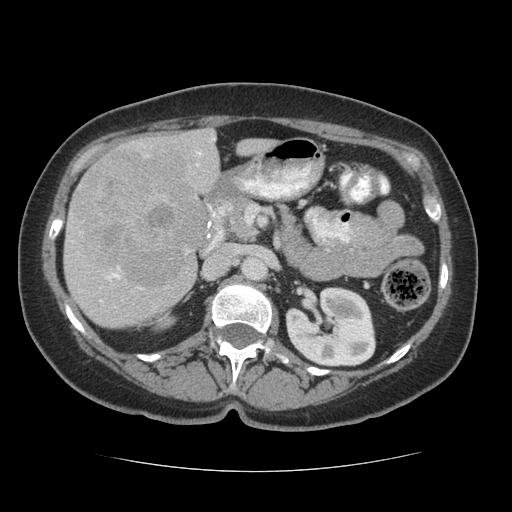
Contrast-enhanced abdominal CT (liver protocol), one axial slice; reconstruction kernel STANDARD; 140 kVp; soft-tissue window (W 400 / L 40 HU); 2.5 mm slice thickness; 512 × 512 image matrix. Case-level facts recorded for this patient, not image findings: diagnosis: hepatocellular carcinoma (patient treated with transarterial chemoembolisation; whether this scan precedes or follows treatment is not stated here); TNM stage (as recorded): Stage-I; Child-Pugh class: A; tumour differentiation: moderately differentiated; tumour nodularity: uninodular.
Outlined on this slice (semi-automatic segmentation, software-assisted and operator-edited):
- liver parenchyma outside the tumour (the mass and vessels are separate outlines, so this box may not span the whole liver): bounding box <64,128,276,326> (left, top, right, bottom; pixels)
- mass: <68,147,208,292>
- liver vessels: <100,138,215,302>